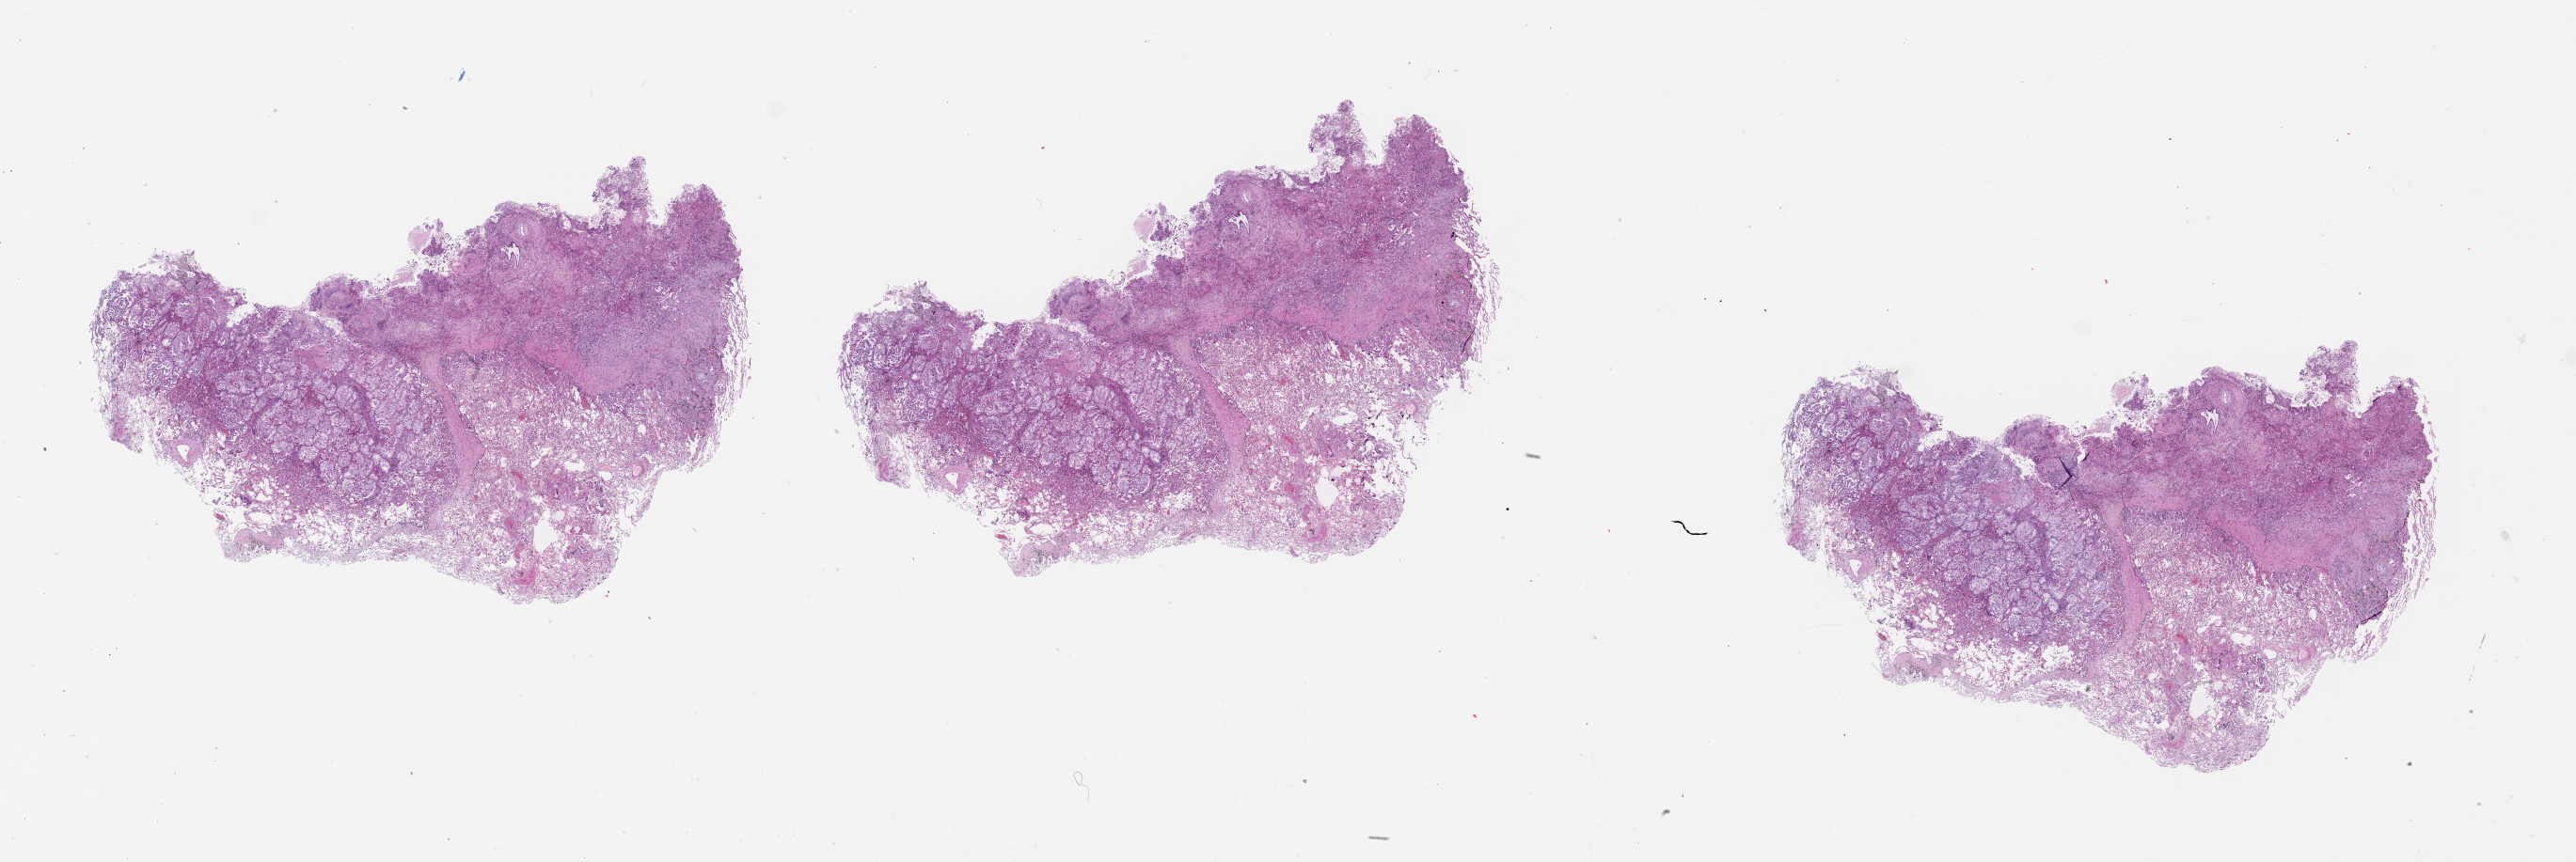
Hematoxylin and eosin (H&E) stained whole-slide image, shown as a low-resolution overview of the whole scanned area (about 44.1 x 14.8 mm). Lung, tissue type not recorded.
Patient diagnosis (cohort enrolment): lung adenocarcinoma (lung).